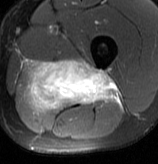
MRI of an extremity soft-tissue mass, one axial slice; slice 44 of 70 in the series (ordered by position); T2-weighted fat-saturated; MR volume resampled by the dataset authors to the PET/CT grid (not the native acquisition matrix); 3.27 mm slice thickness; 158 × 164 image matrix, field of view 154 × 160 mm. Male patient. From the clinical record (not read from this slice): histological type: extraskeletal osteosarcoma; grade: high; site of the primary tumour: left adductur.
Outlined on this slice (expert contour drawn on MRI and transferred to this co-registered scan by the dataset authors):
- gross tumour volume (mass): bounding box (x1, y1, x2, y2) in pixels: (24, 60, 121, 111)